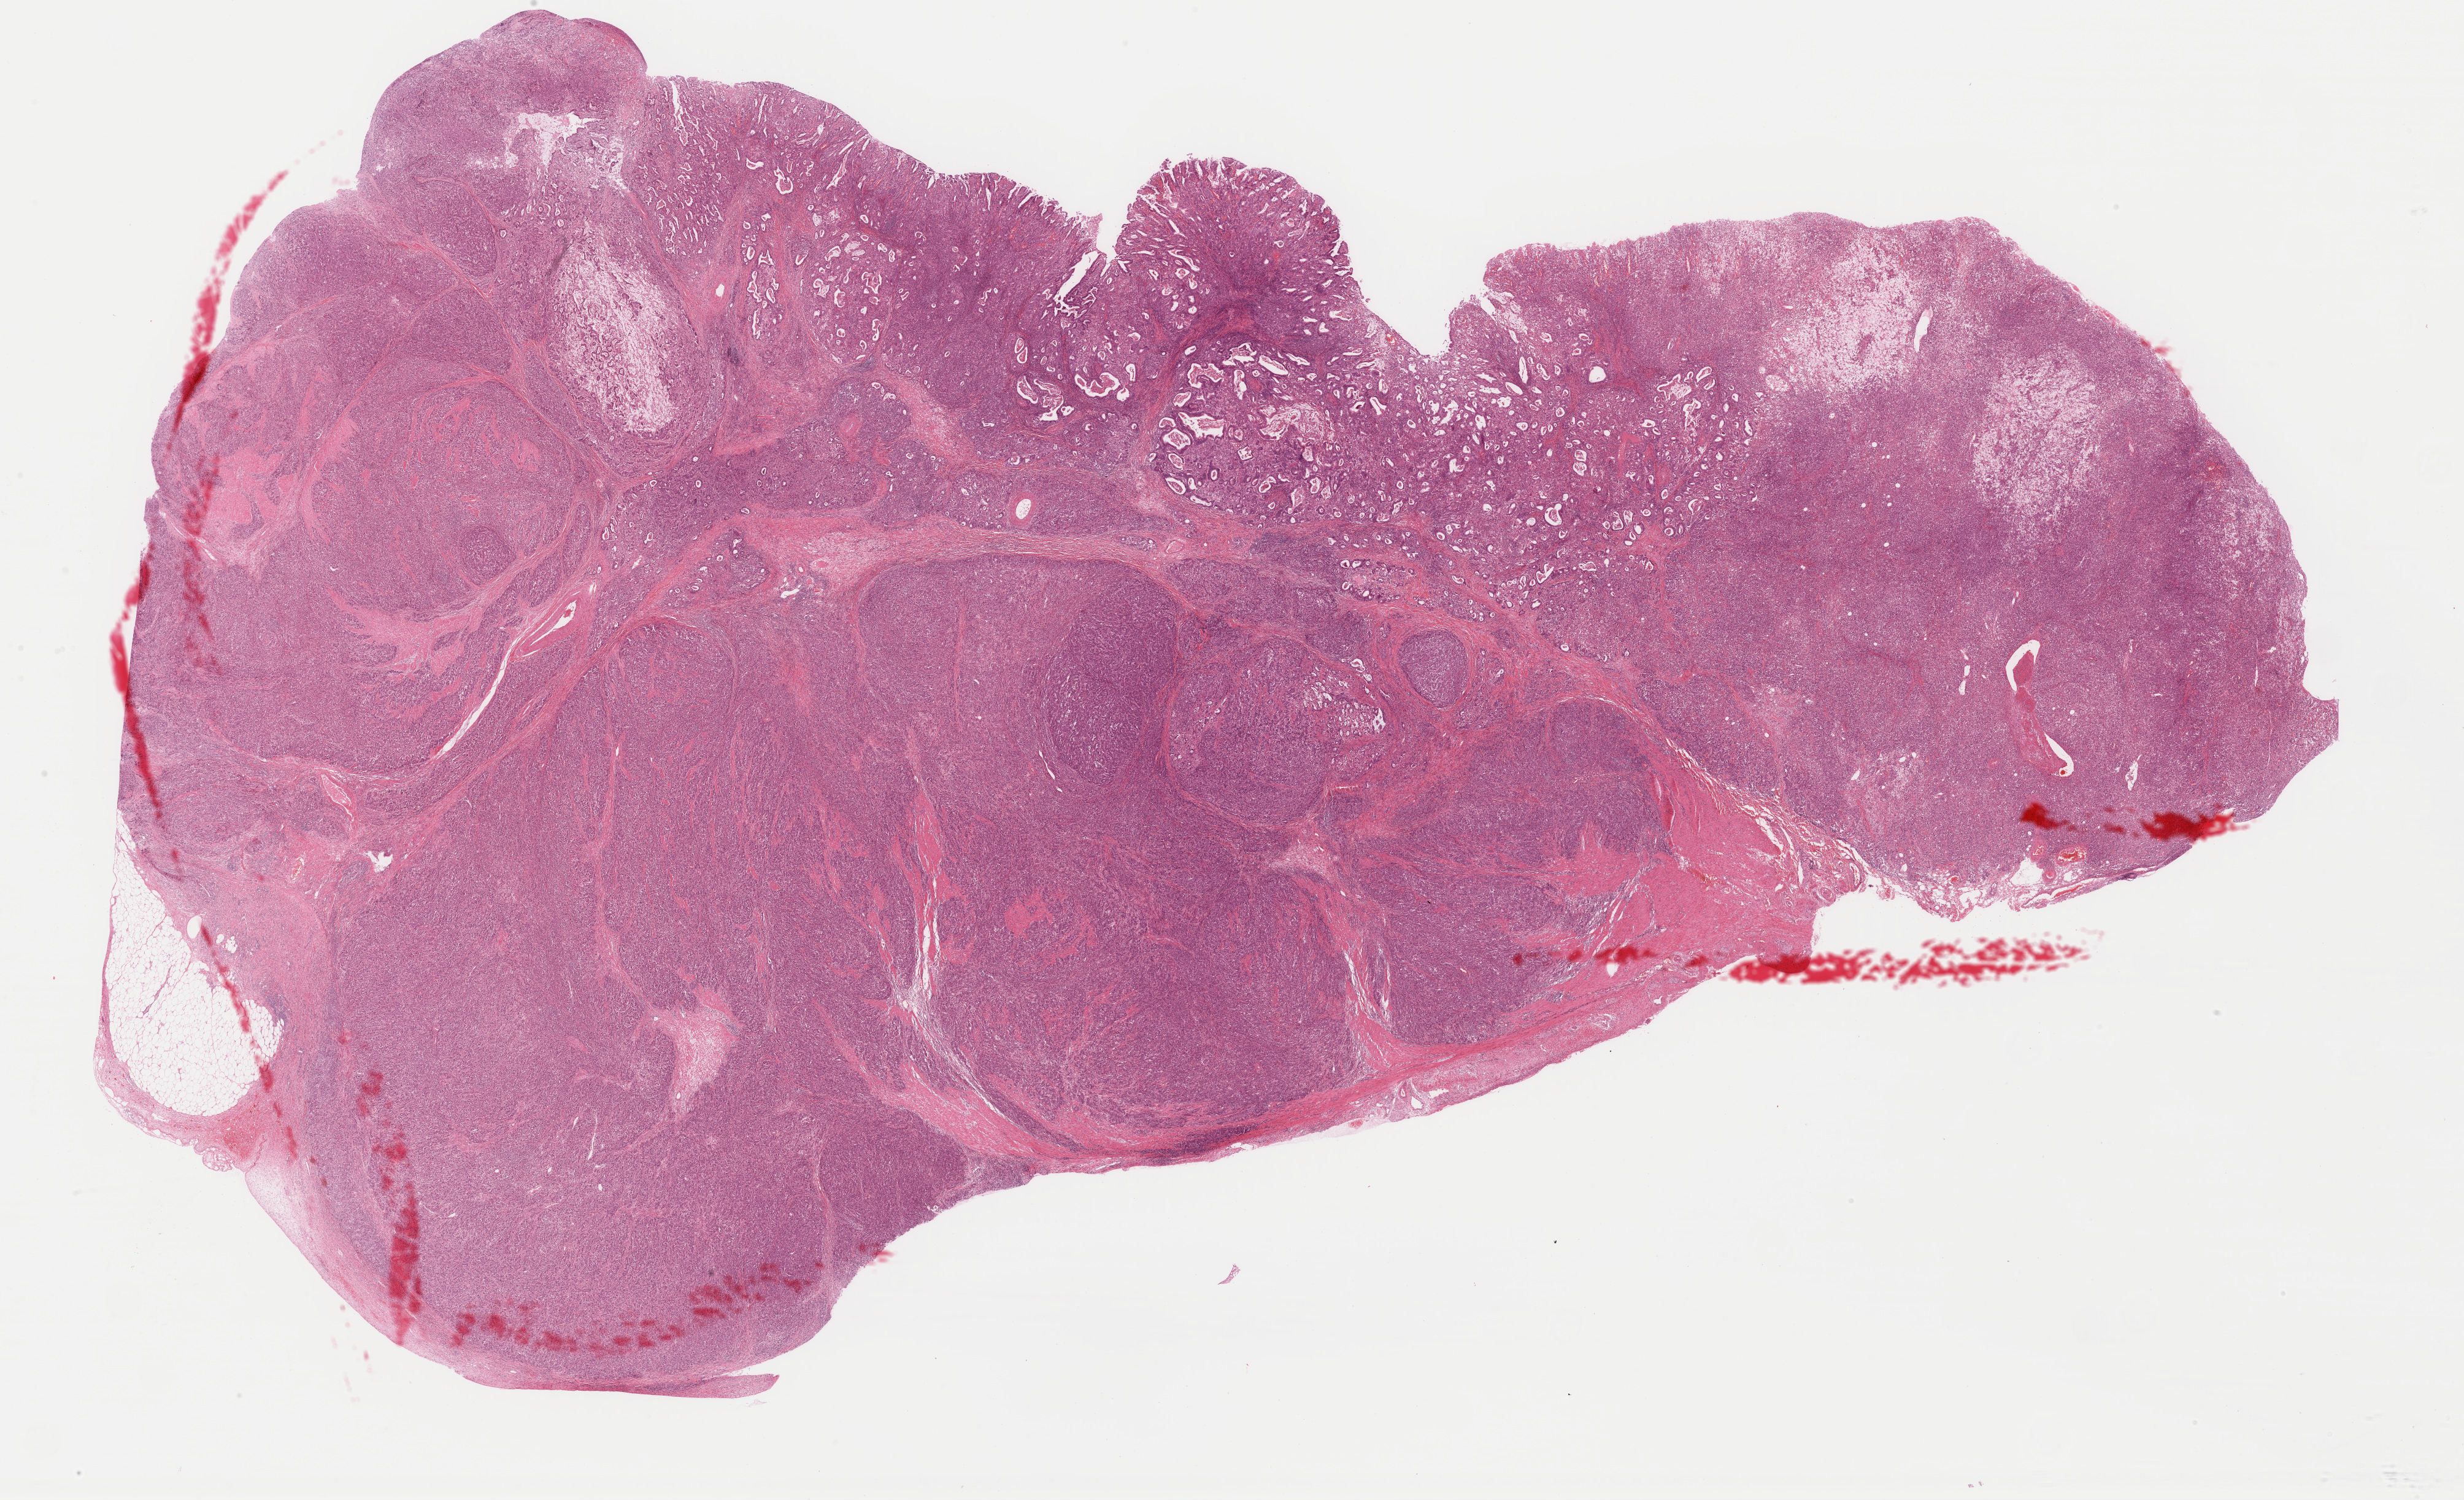
Whole-slide histology image, H&E-stained, shown as a low-resolution overview of the whole scanned area (about 31.7 x 19.3 mm), formalin-fixed paraffin-embedded (FFPE) diagnostic section, esophagus, primary tumour sample. Male patient; age at initial diagnosis 71 years. Histologic grade: G3 (poorly differentiated).
* lymph nodes positive (case pathology): 6 of 6 examined
* AJCC pathologic stage: IIIB (7th edition)
* pathologic diagnosis: Adenocarcinoma, NOS (thoracic esophagus)